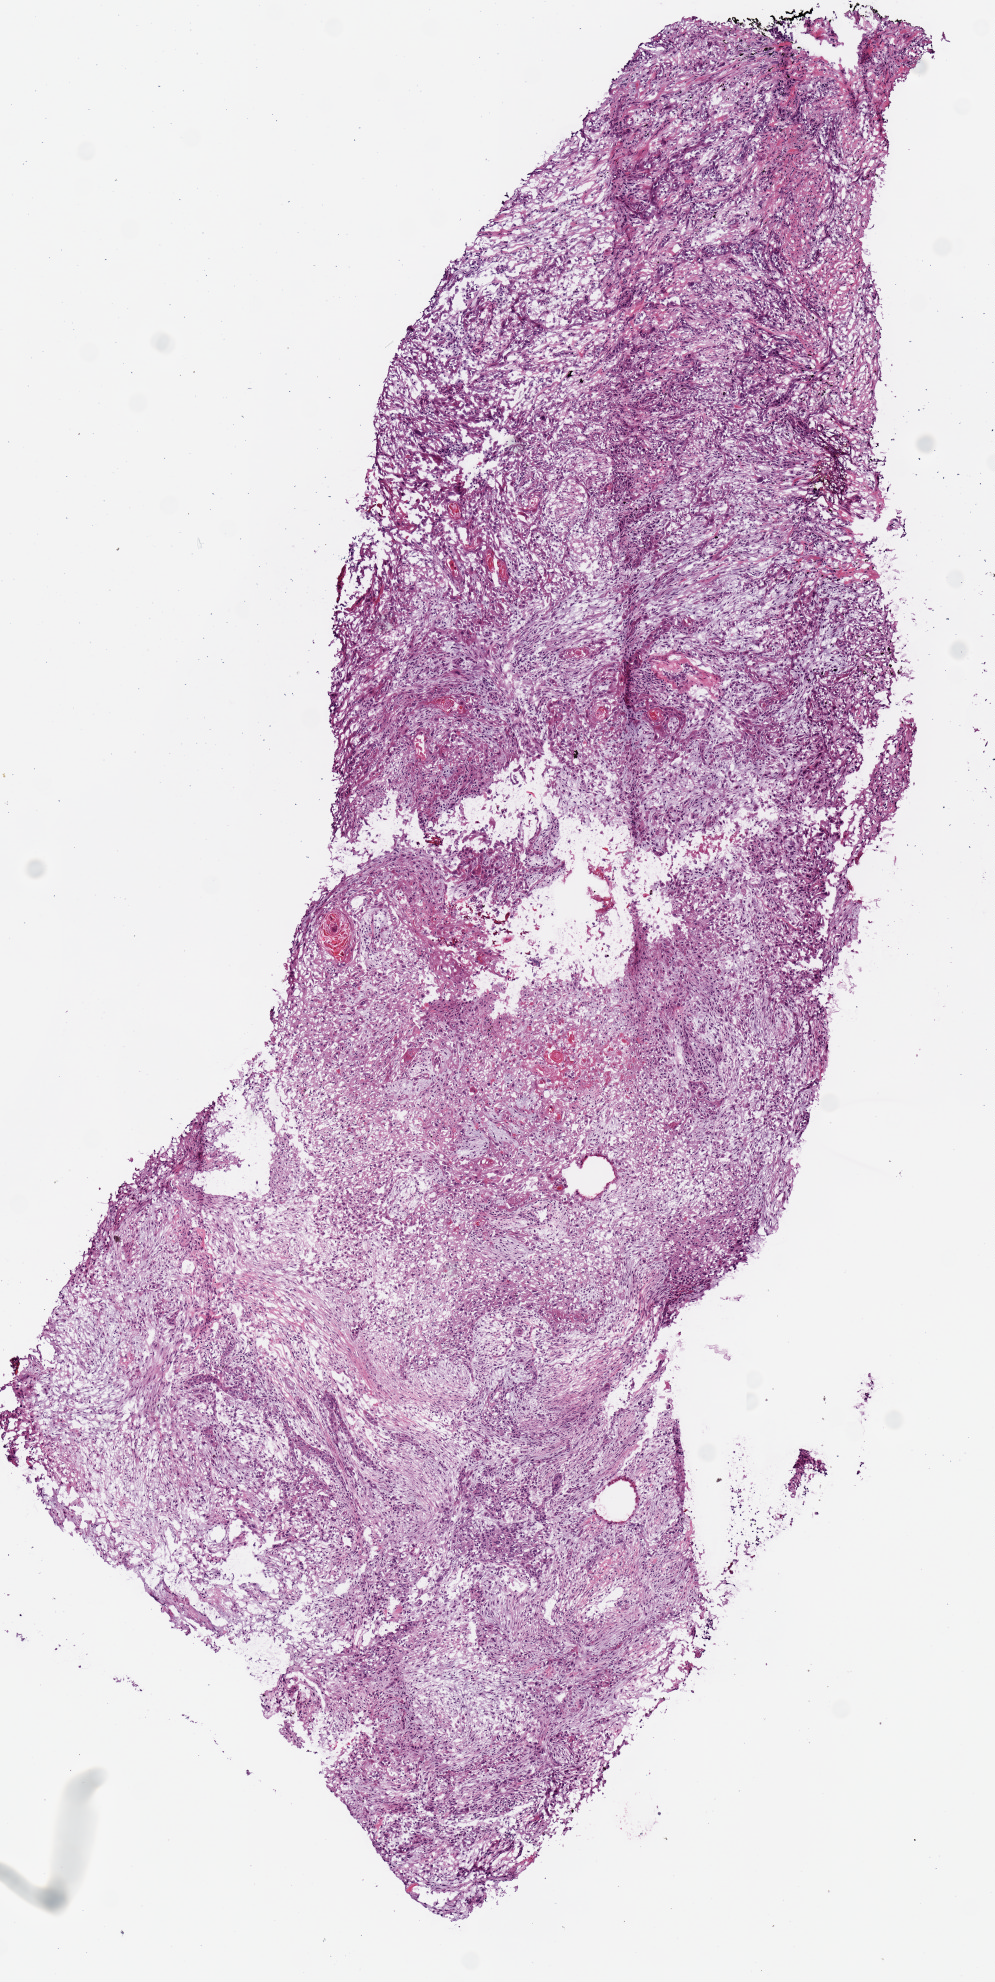
Hematoxylin and eosin (H&E) stained whole-slide image — low-resolution overview of the scanned area, about 3.9 x 7.8 mm, frozen section from the bottom of the tissue portion, sample: primary tumour, lung. Patient: male, age at initial diagnosis 69 years.
* AJCC pathologic stage: IIB (6th edition)
* pathologic diagnosis: Squamous cell carcinoma, NOS